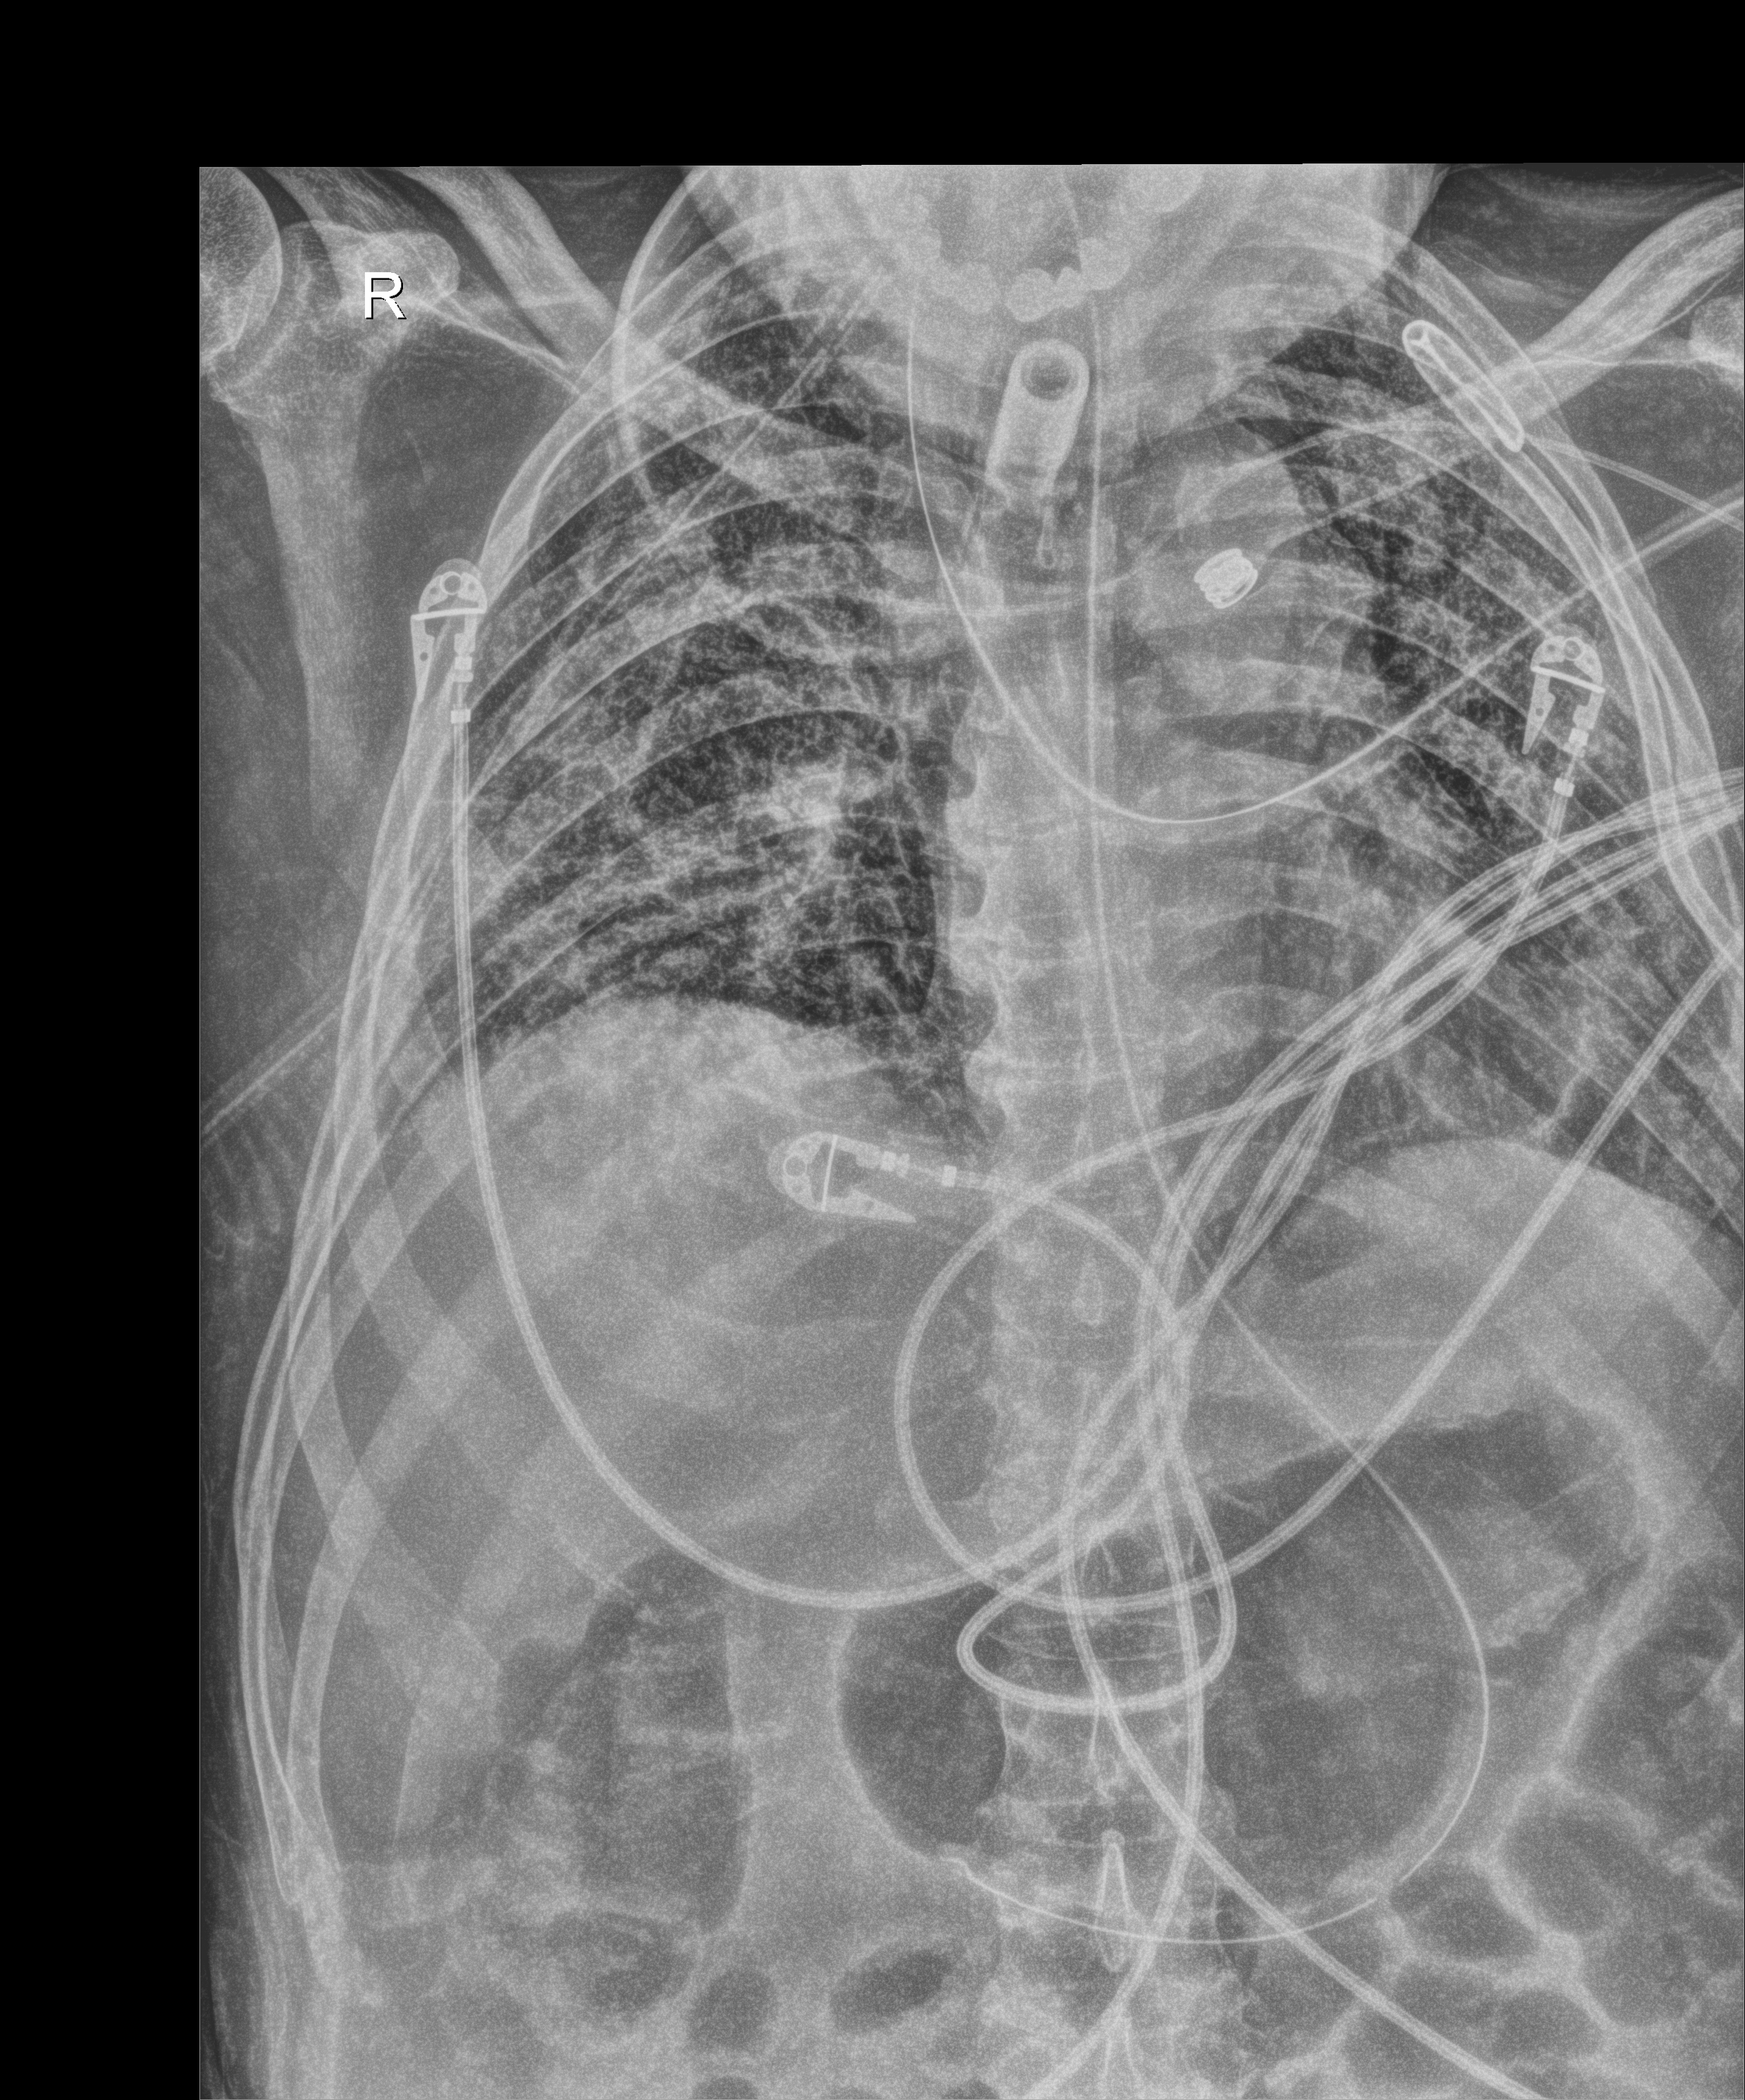
Chest X-ray (portable); anteroposterior (AP) projection. Male patient hospitalised with COVID-19, age 18–59 years.
From the hospital-stay record, not from the radiograph (when in the stay this image was taken is not recorded):
- admitted to intensive care during this hospital stay: yes
- smoking status (admission record): never